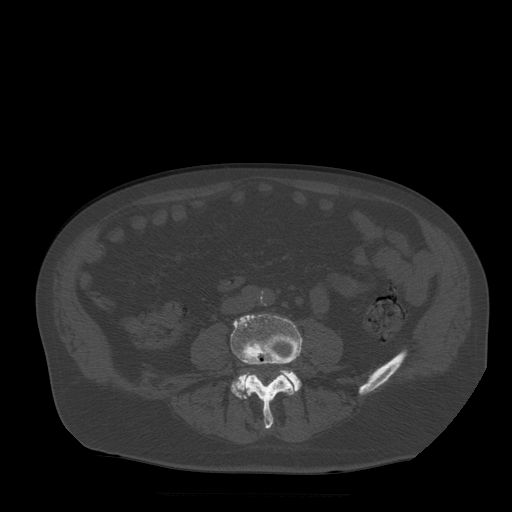
CT including the spine, one axial slice. Slice 108 of 522 in the series (ordered by position). Bone window (W 1800 / L 400 HU). 512 × 512 image matrix, field of view 420 × 420 mm. Patient age 72 years. Case-level facts recorded for this patient, not image findings: primary cancer: prostate.
Structures marked on this image (semi-automatically segmented with operator editing):
- L4 vertebra: bounding box (x1, y1, x2, y2) in pixels: (231, 315, 303, 429)
- L5 vertebra: (232, 370, 301, 400)